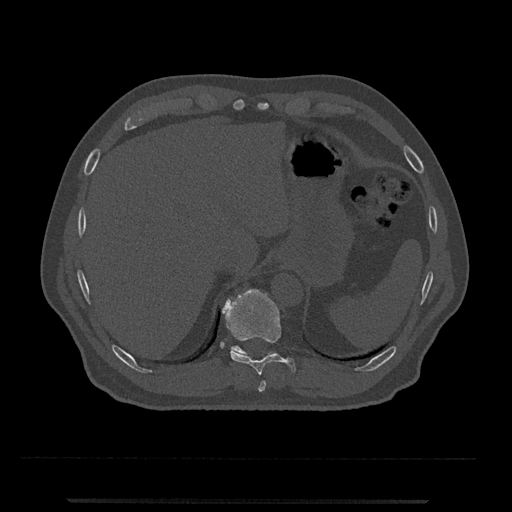
CT including the spine, one axial slice. Position 508 of 797 along the scan axis. Reconstruction kernel Br40s/3. Bone window (W 1800 / L 400 HU). 0.5 mm slice thickness. 512 × 512 image matrix, field of view 419 × 419 mm. Male patient, age 63 years. Case-level facts recorded for this patient, not image findings: primary cancer: prostate.
Annotated regions visible in this slice (semi-automatically segmented with operator editing):
- T10 vertebra: bounding box [x1, y1, x2, y2] px = [222, 289, 296, 375]
- T11 vertebra: [231, 346, 274, 356]
- T9 vertebra: [258, 381, 266, 392]